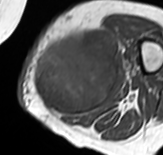
MRI of an extremity soft-tissue mass, one axial slice. Position 26 of 65 along the scan axis. MR volume resampled by the dataset authors to the PET/CT grid (not the native acquisition matrix). 3.27 mm slice thickness. 163 × 155 image matrix. Female patient. Case-level facts recorded for this patient, not image findings: histological type: pleomorphic leiomyosarcoma; grade: high; site of the primary tumour: left thigh.
Outlined on this slice (expert contour drawn on MRI and transferred to this co-registered scan by the dataset authors):
- gross tumour volume including surrounding oedema: box from (x=33, y=31) to (x=120, y=116) px
- gross tumour volume (mass): (x=33, y=33)–(x=118, y=116)